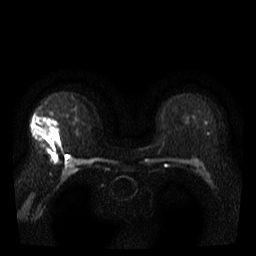
Breast MRI, one axial slice; position 25 of 40 along the scan axis; diffusion-weighted series; image 2 of 4 stored at this slice position (different b-values; order by instance number); 3 T; 5 mm slice thickness; 256 × 256 image matrix, field of view 300 × 300 mm. Female patient.
Structures marked on this image (outlined manually by an expert reader):
- tumour on diffusion-weighted imaging: bounding box [x1, y1, x2, y2] px = [43, 119, 60, 142]